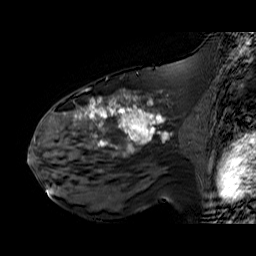
Breast MRI (dynamic contrast-enhanced), one sagittal slice. Position 34 of 60 along the scan axis. Dynamic contrast-enhanced series, time point 2 of 6 at this slice position (early post-contrast). 1.5 T. TE 6.3 ms, TR 32.9 ms. 256 × 256 image matrix, field of view 200 × 200 mm. Female patient. Case-level facts recorded for this patient, not image findings: setting: breast cancer imaged before/during neoadjuvant chemotherapy; receptor status: HER2-positive.
Structures marked on this image (semi-automatically segmented with operator editing):
- analysis volume of interest (the breast-tissue region the enhancement analysis was run in; not a lesion): box from (x=48, y=92) to (x=195, y=174) px
- tumour enhancement mask (voxels above the 100 % enhancement threshold inside the analysis volume of interest): (x=73, y=95)–(x=163, y=151)